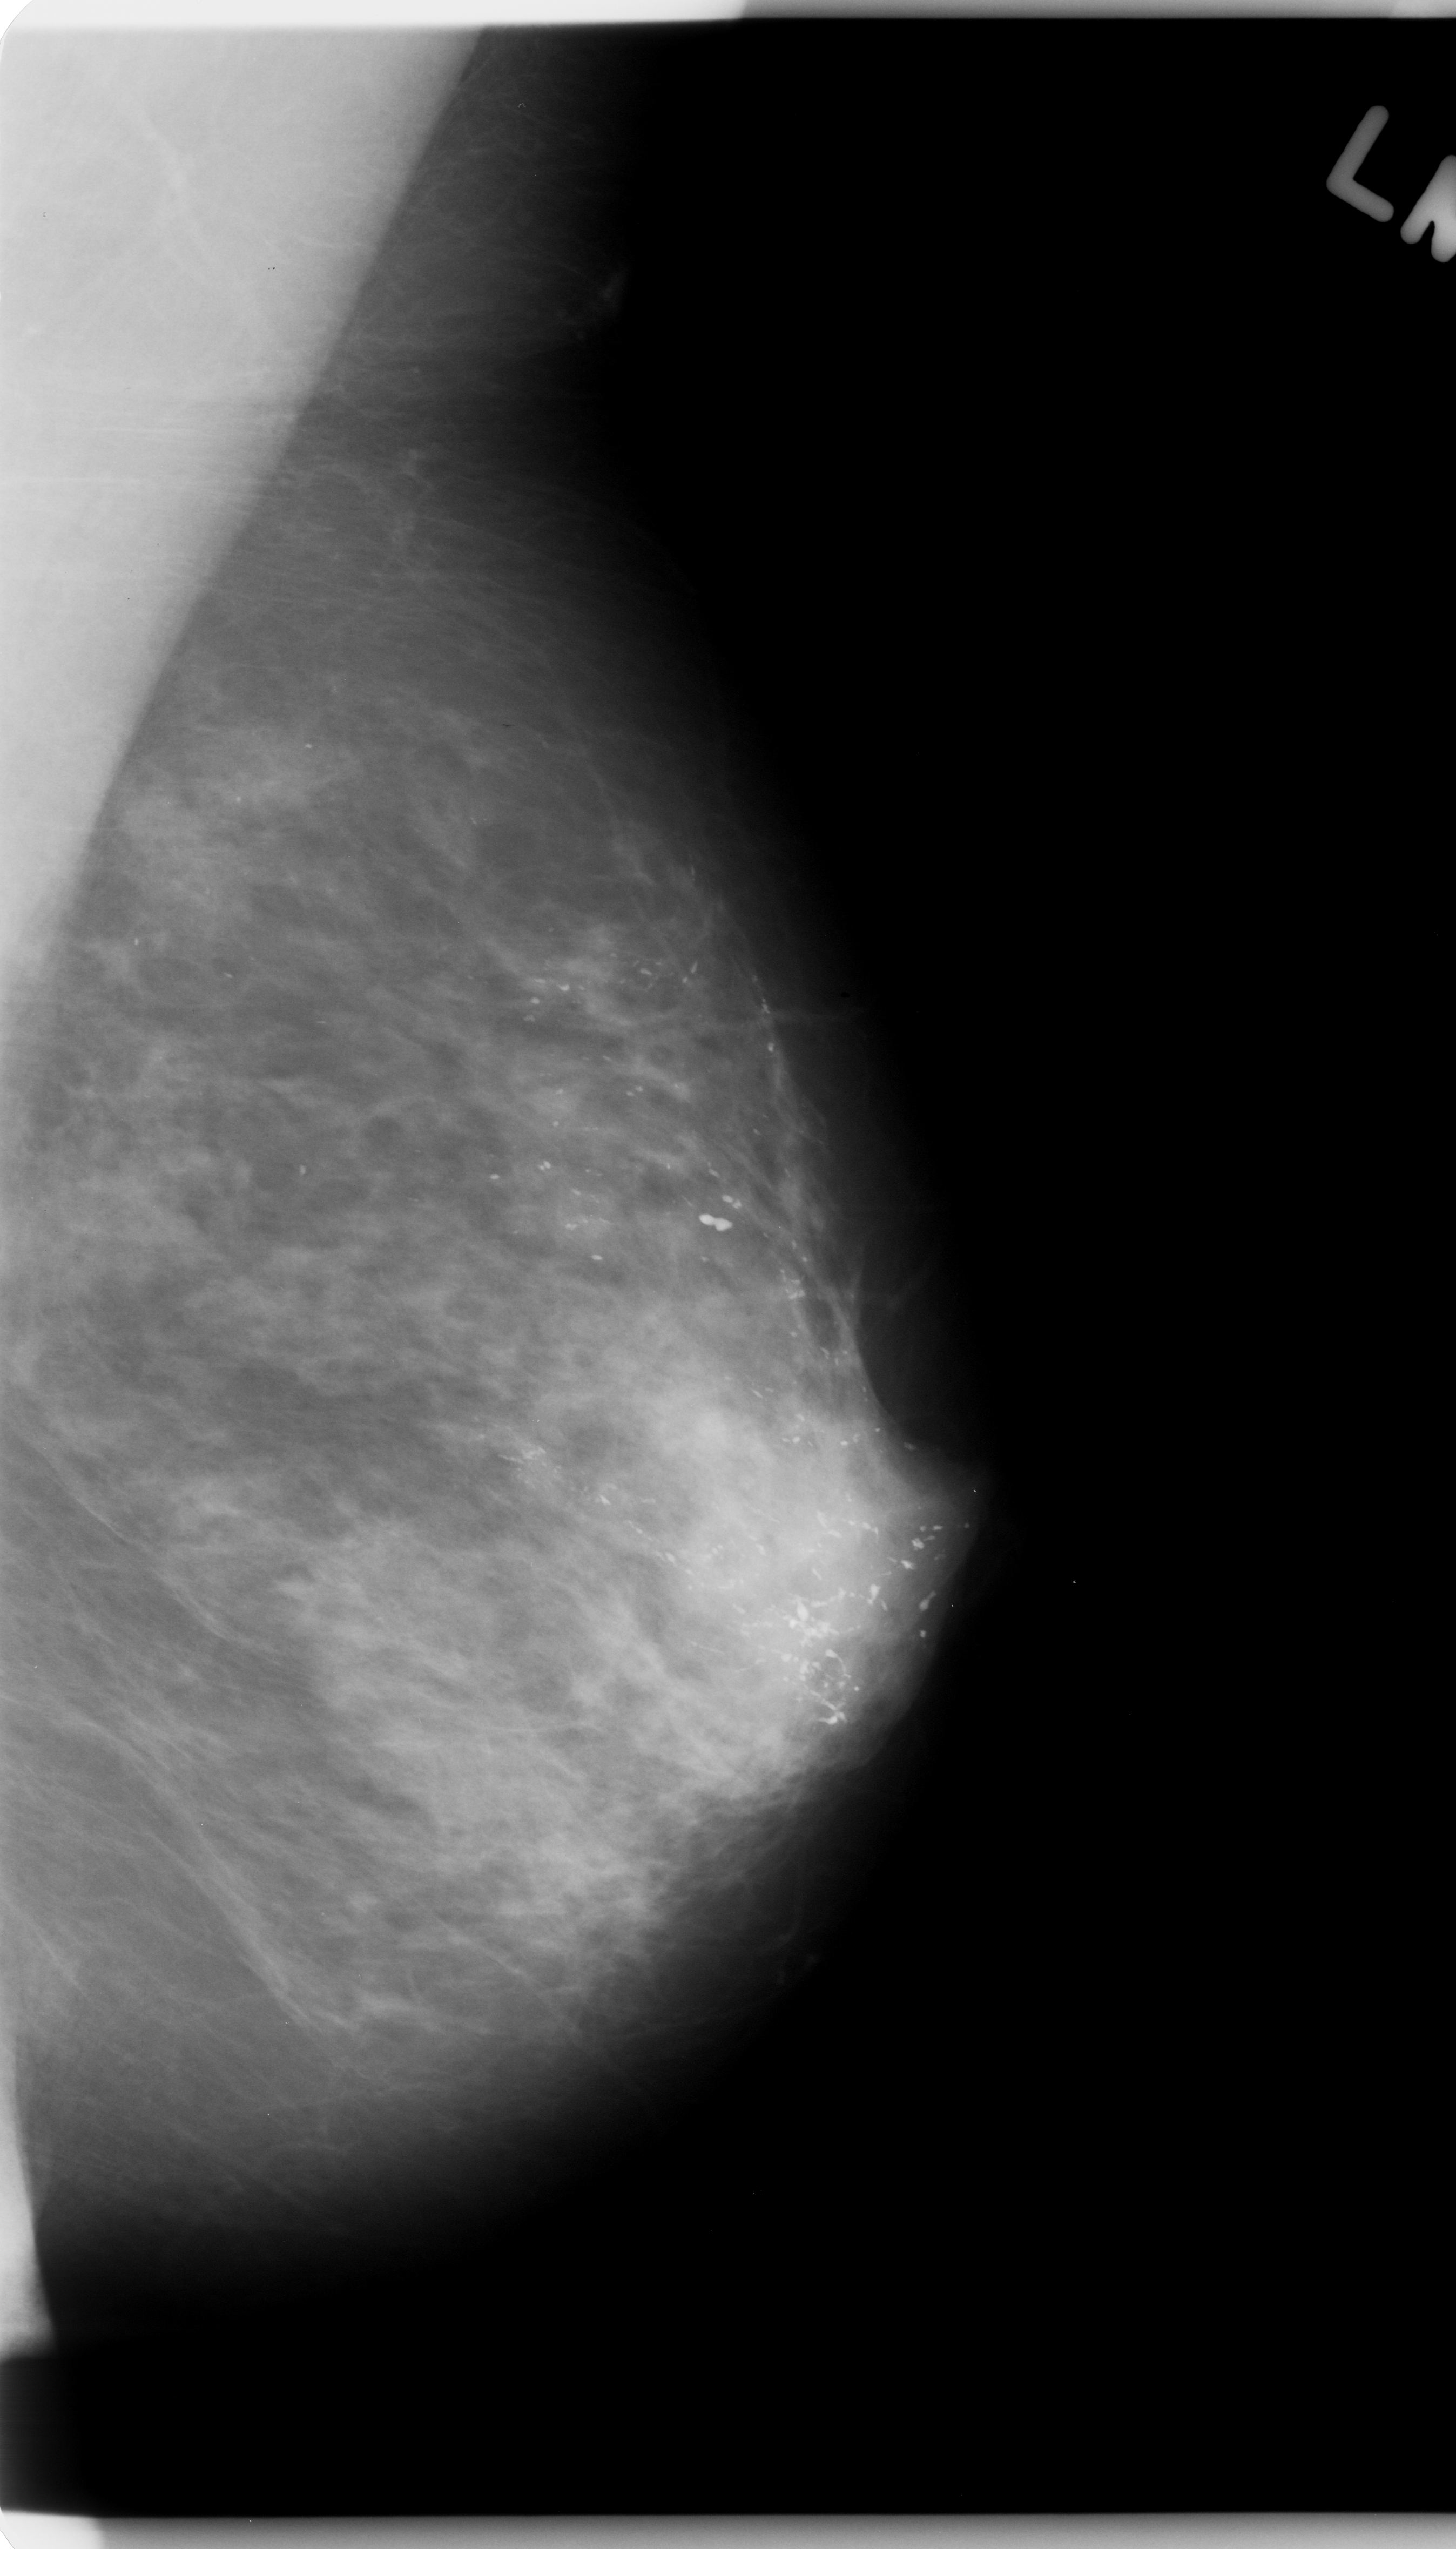
Mammogram (digitized film), left breast, MLO view, breast composition: heterogeneously dense (BI-RADS density category 3 of 4).
- Calcifications, morphology fine linear branching, distribution regional; BI-RADS assessment category 5; subtlety rating 5 on a 1 (subtle) to 5 (obvious) scale; pathology result (as recorded, not read from the image): malignant.